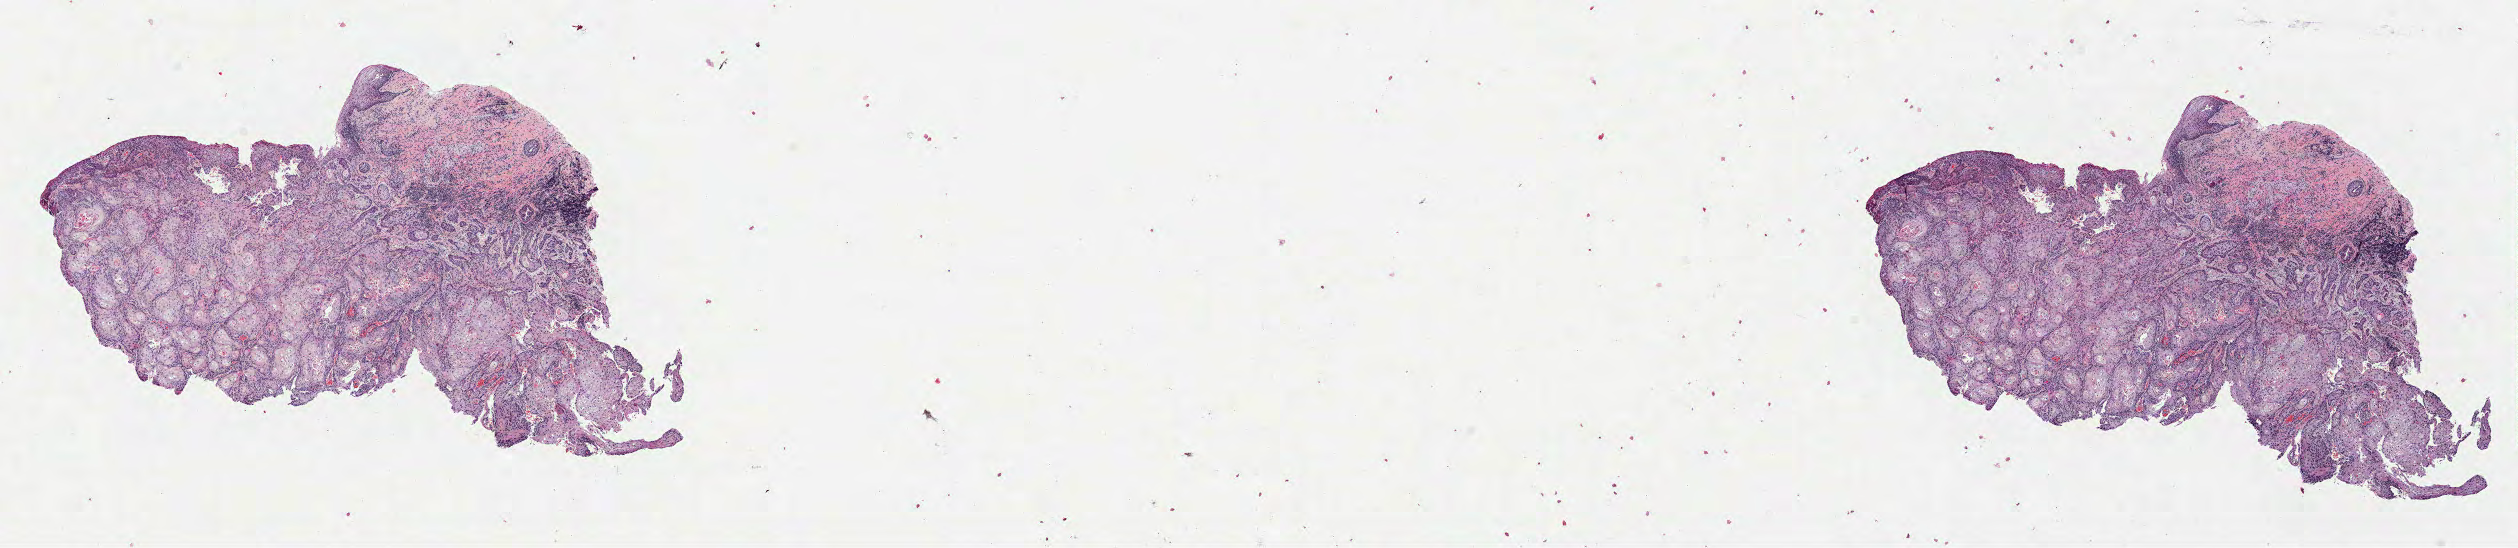
Digitized H&E-stained tissue section (whole slide) — a low-resolution overview of the entire scanned area, about 20.3 x 4.4 mm (acquisition: 40x scan), formalin-fixed paraffin-embedded (FFPE) diagnostic section, sample: primary tumour, head and neck. Female patient; age at initial diagnosis 63 years. Histologic grade: G2 (moderately differentiated).
- pathologic diagnosis: Squamous cell carcinoma, NOS (larynx, NOS)